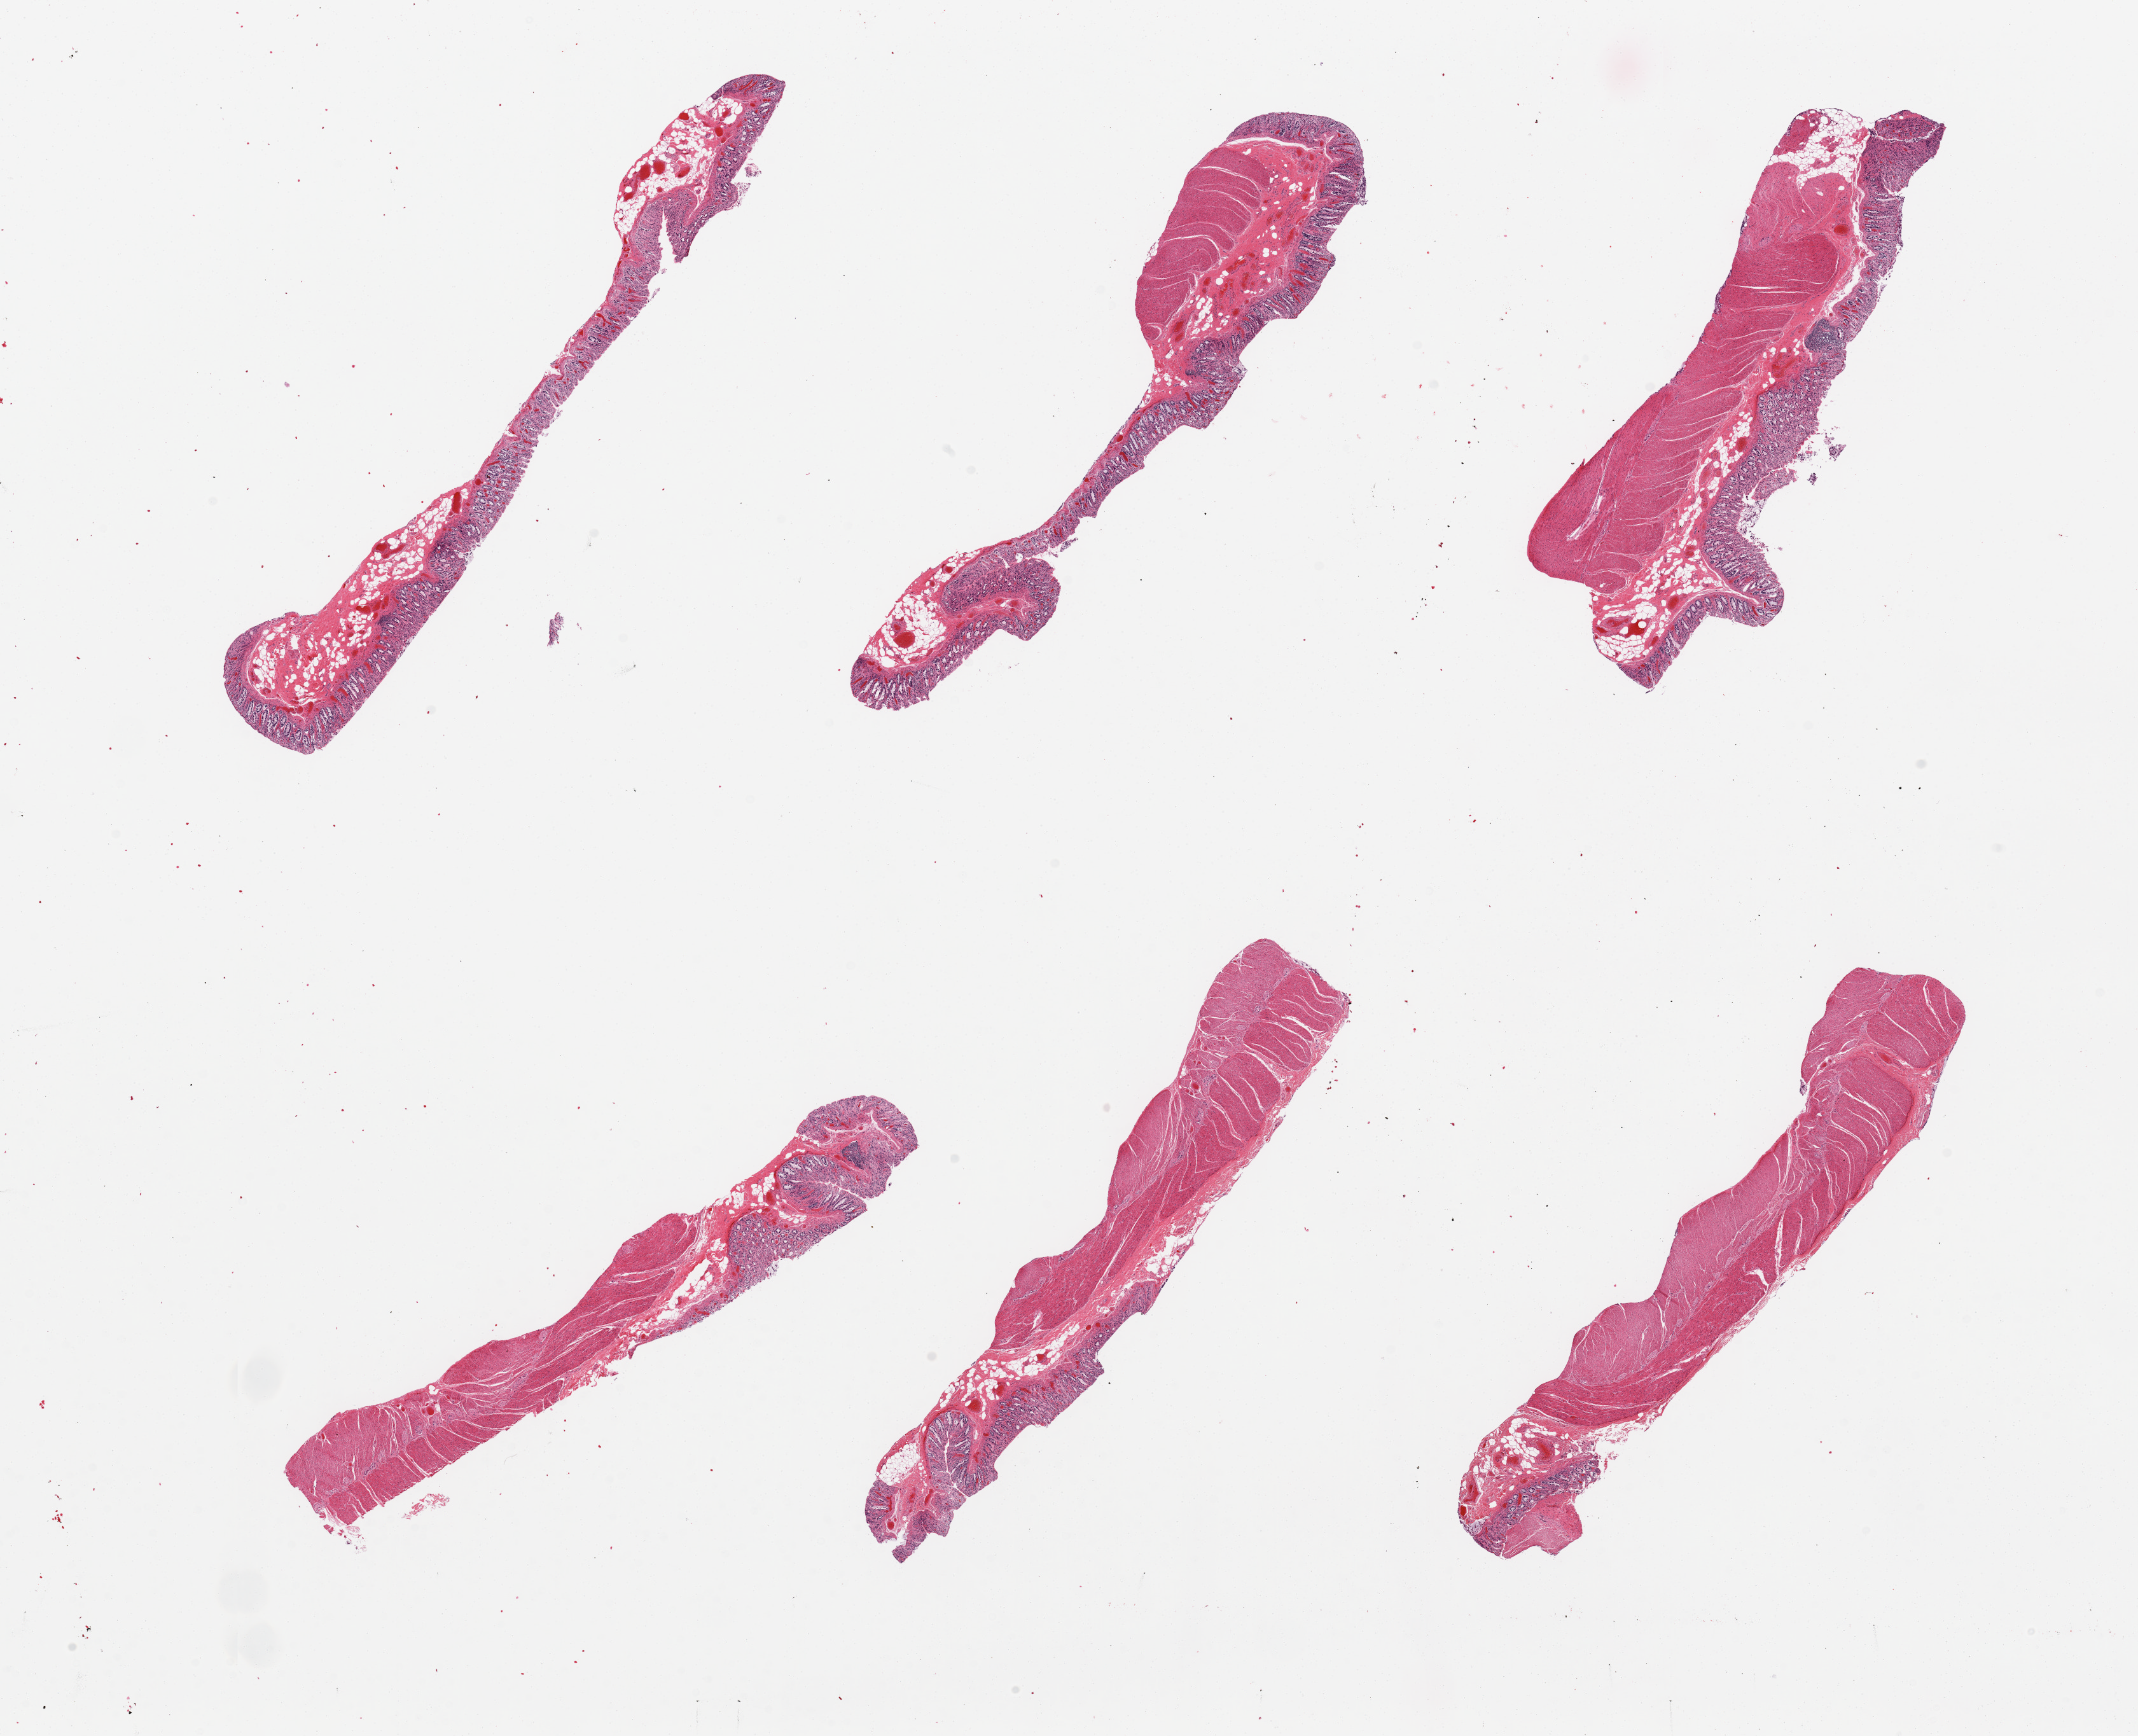
Whole-slide image, H&E stain — low-resolution overview of the scanned area, about 26.6 x 21.6 mm. PAXgene-fixed, paraffin-embedded tissue. Section of transverse colon (target tissue). Donor tissue sample.
Reviewer comment on this tissue sample: 6 pieces, mucosa near-total autolysis.